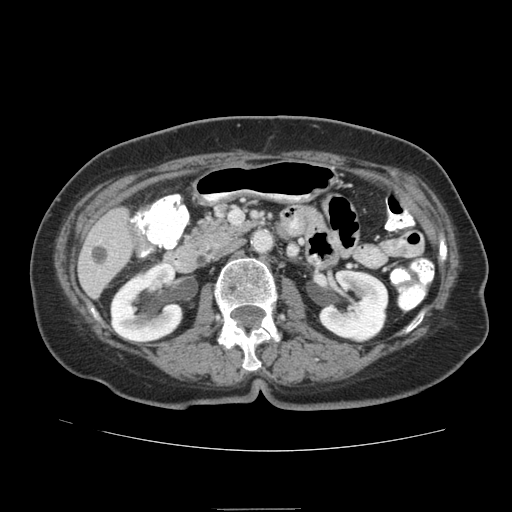
Contrast-enhanced abdominal CT (liver protocol), one axial slice; 140 kVp; soft-tissue window (W 400 / L 40 HU); 2.5 mm slice thickness; 512 × 512 image matrix, field of view 360 × 360 mm. Case-level facts recorded for this patient, not image findings: diagnosis: hepatocellular carcinoma (patient treated with transarterial chemoembolisation; whether this scan precedes or follows treatment is not stated here); TNM stage (as recorded): Stage-IVA; Child-Pugh class: B; tumour nodularity: uninodular.
Outlined on this slice (semi-automatic segmentation, software-assisted and operator-edited):
- liver parenchyma outside the tumour (the mass and vessels are separate outlines, so this box may not span the whole liver): bounding box [x1, y1, x2, y2] px = [78, 208, 134, 298]